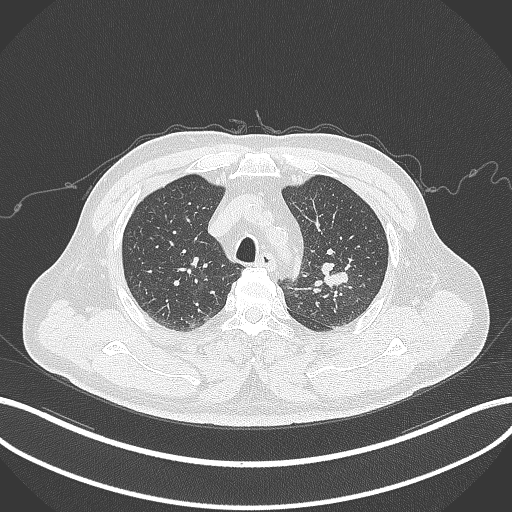
Chest CT, one axial slice; position 238 of 286 along the scan axis; lung window (W 1500 / L -600 HU); 512 × 512 image matrix, field of view 400 × 400 mm. Male patient, age 67 years. From the clinical record (not read from this slice): clinical TNM (as recorded): T2a N1 M0.
Annotated regions visible in this slice (rectangle marked by the reading radiologist):
- lung tumour (recorded histology: adenocarcinoma): box from (x=319, y=258) to (x=351, y=291) px